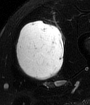
MRI of an extremity soft-tissue mass, one axial slice. Position 32 of 65 along the scan axis. T2-weighted fat-saturated. MR volume resampled by the dataset authors to the PET/CT grid (not the native acquisition matrix). 90 × 105 image matrix, field of view 88 × 103 mm. Male patient. Case-level facts recorded for this patient, not image findings: histological type: mixoid liposarcoma; grade: low; site of the primary tumour: left thigh.
Annotated regions visible in this slice (expert contour drawn on MRI and transferred to this co-registered scan by the dataset authors):
- gross tumour volume (mass): bounding box <16,21,65,81> (left, top, right, bottom; pixels)